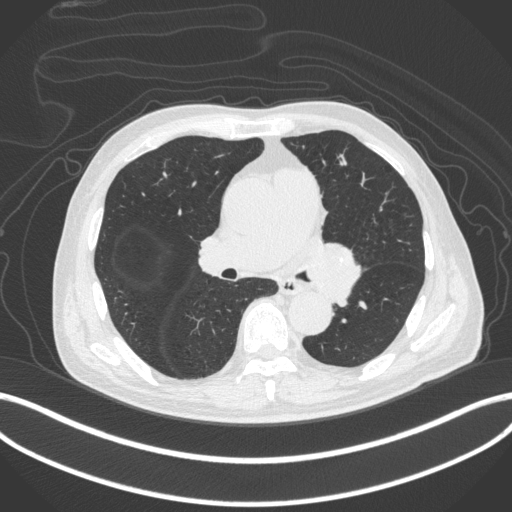
Chest CT, one axial slice. Slice 241 of 420 in the series (ordered by position). 120 kVp. Lung window (W 1500 / L -600 HU). 1 mm slice thickness. 512 × 512 image matrix. Patient: male, 77 years. Case-level facts recorded for this patient, not image findings: clinical TNM (as recorded): T3 N1 M0.
Structures marked on this image (bounding box drawn by a radiologist):
- lung tumour (recorded histology: adenocarcinoma): bounding box <302,237,361,306> (left, top, right, bottom; pixels)